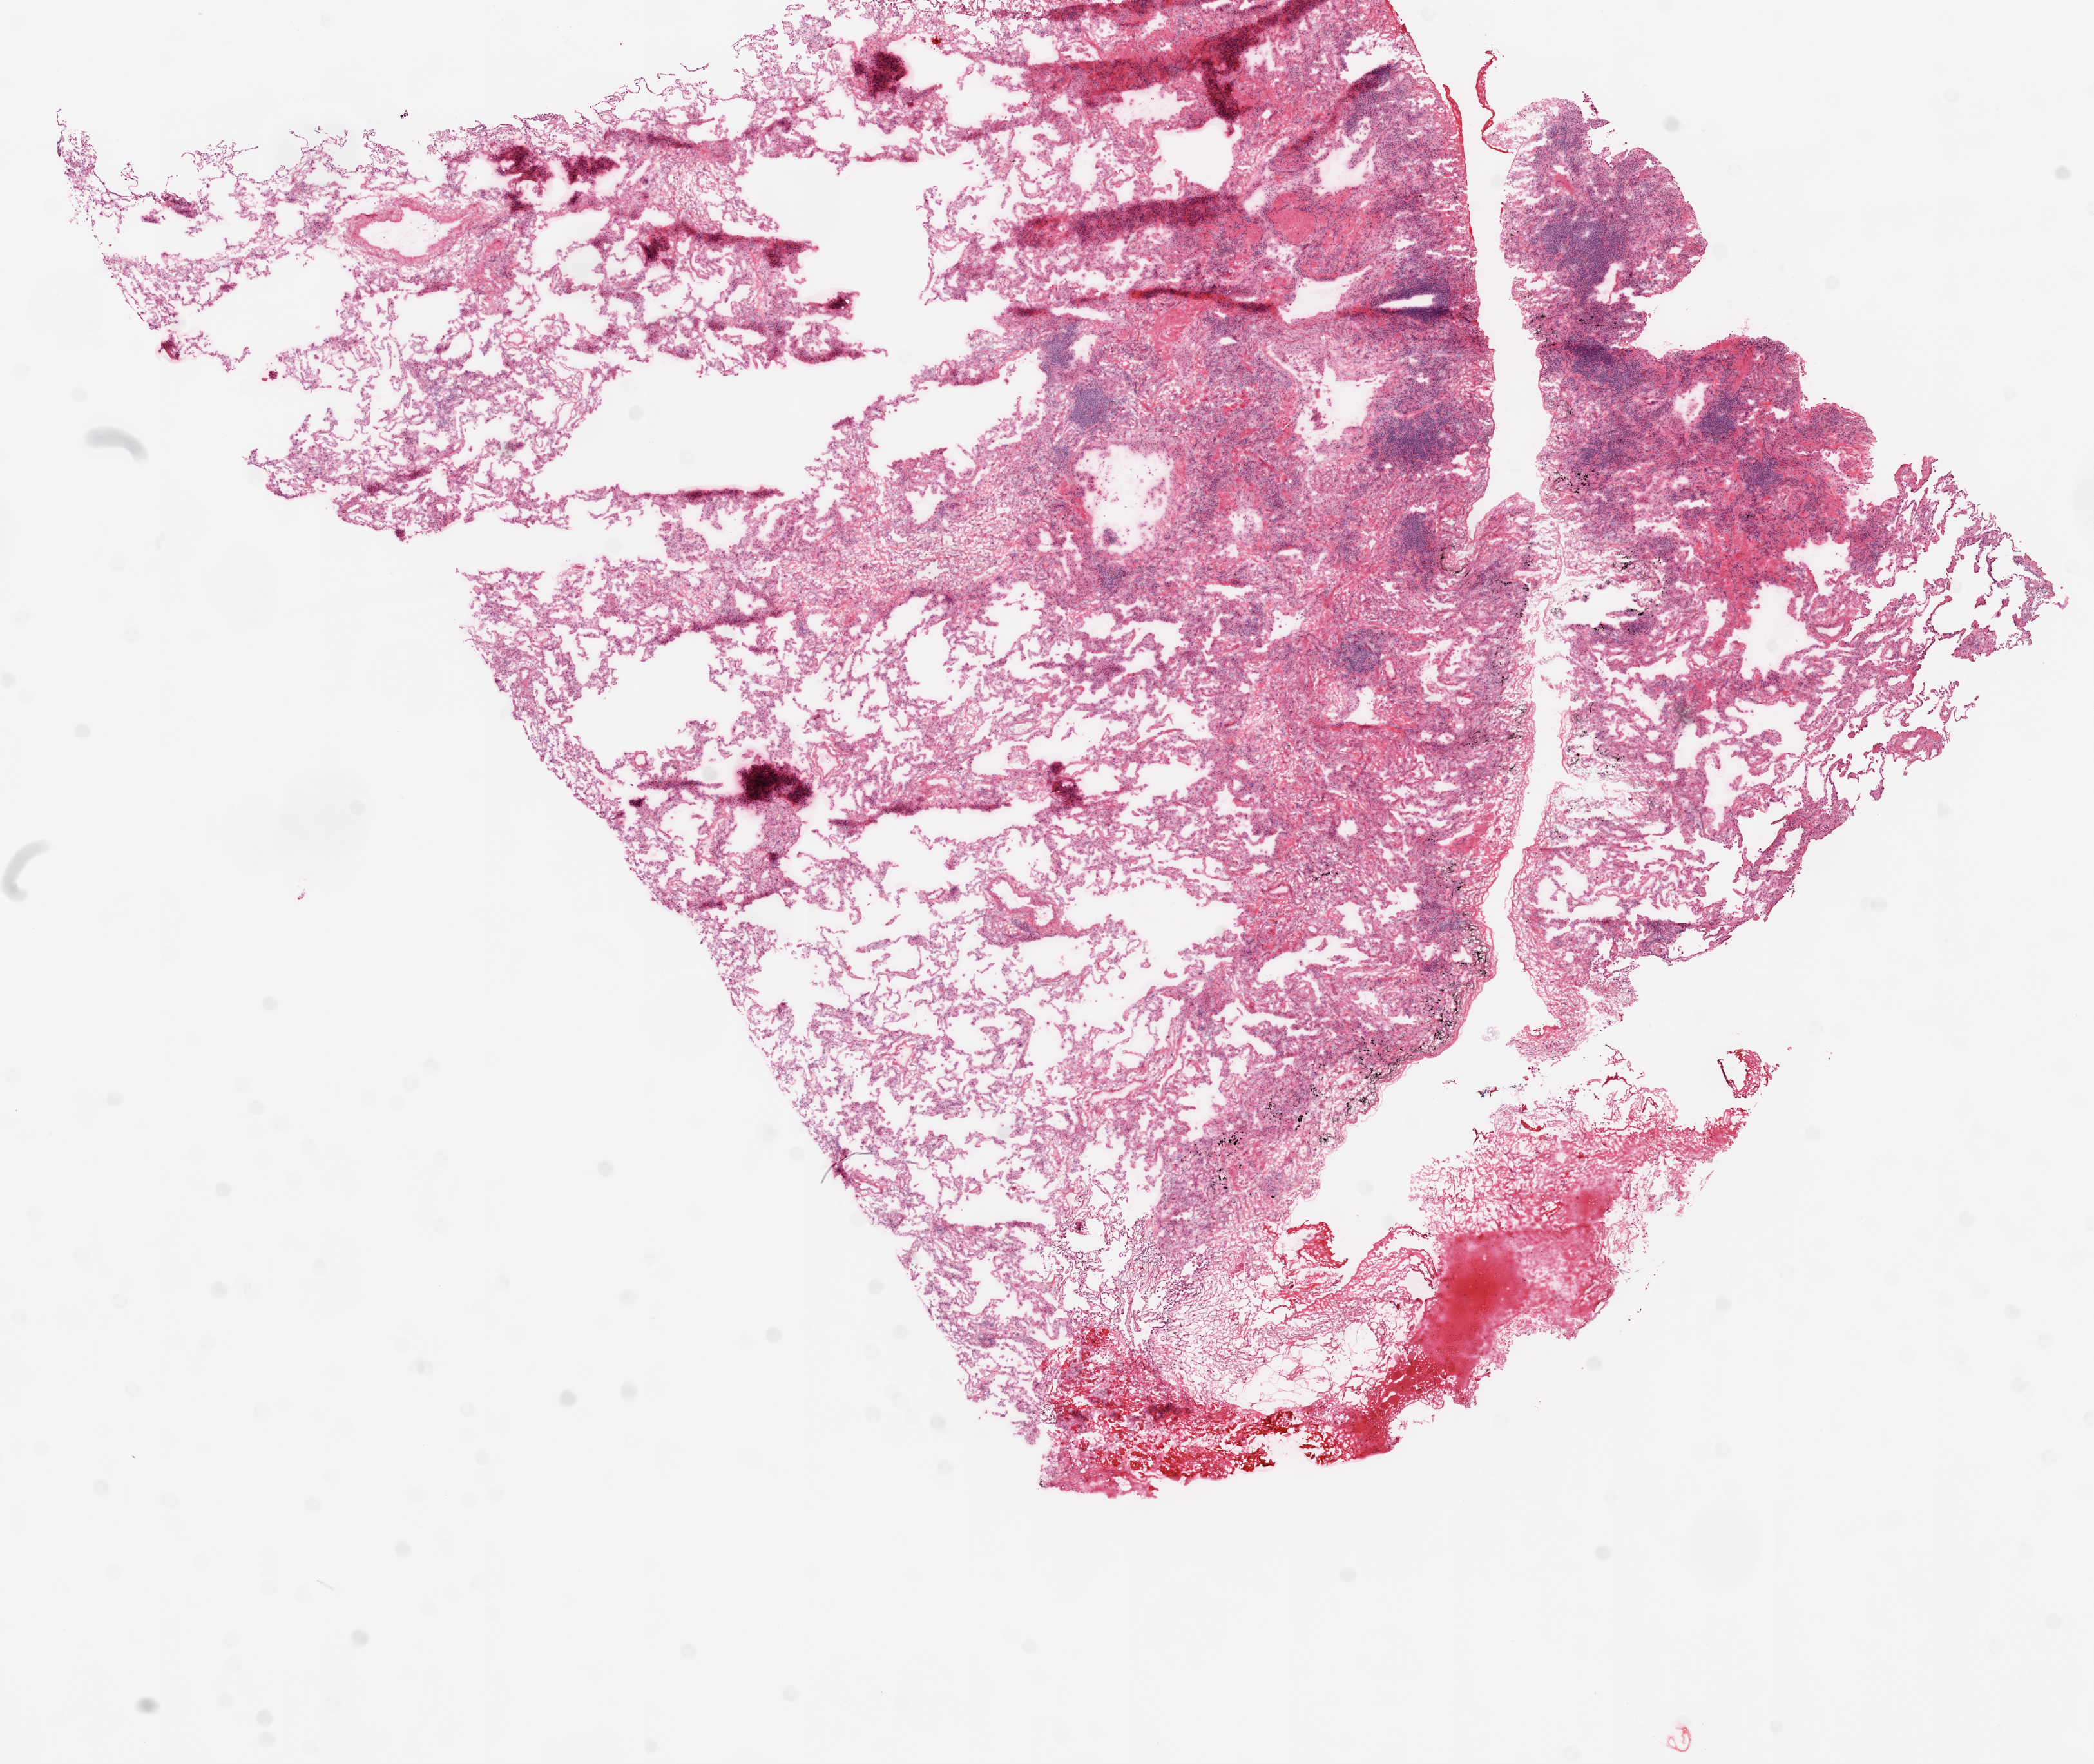
Whole-slide histology image, Hematoxylin and eosin (H&E) stained, a low-resolution overview of the entire scanned area, about 13.0 x 11.0 mm (from a 20x scan). Frozen section from the top of the tissue portion. Lung, solid tissue normal (non-tumour tissue) sample. Male patient; age at initial diagnosis 80 years.
• this section: solid tissue normal sample (biorepository sample class)
• patient diagnosis: Squamous cell carcinoma, NOS